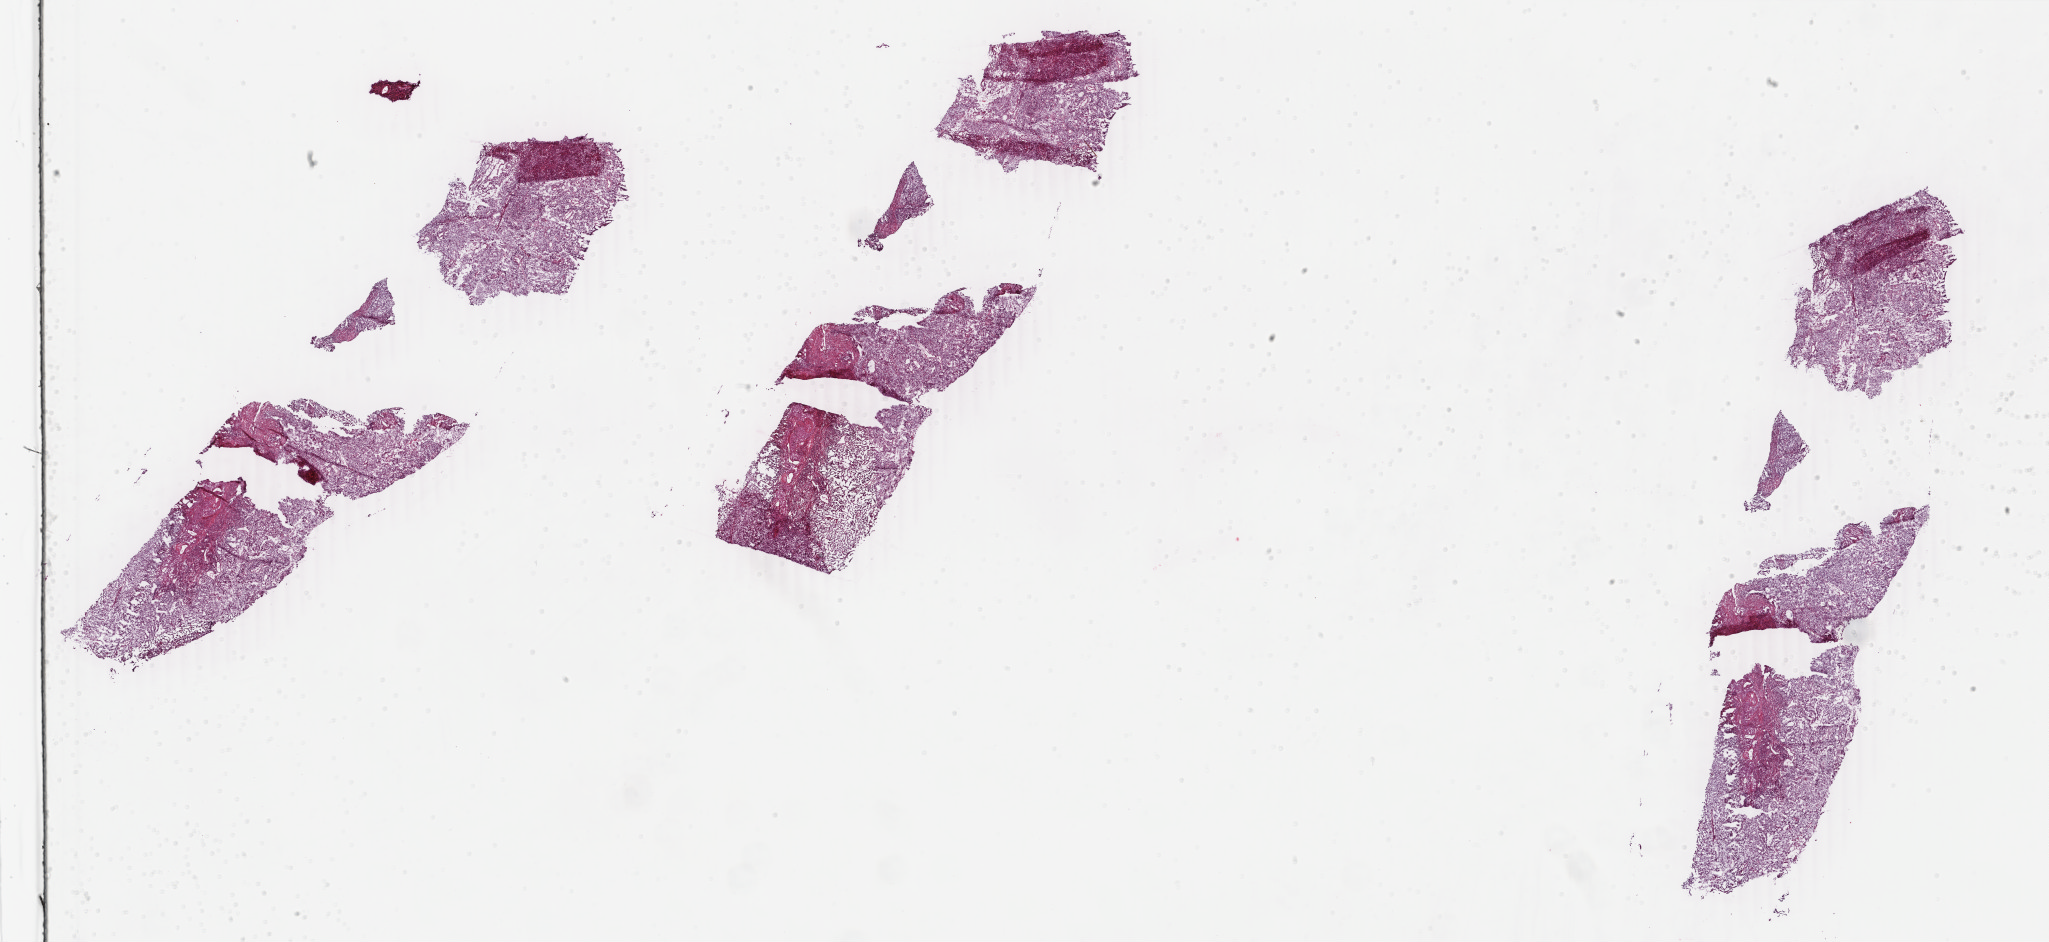
Digitized H&E-stained tissue section (whole slide), whole scanned area (about 32.6 x 15.0 mm) shown as a low-resolution overview. Frozen section. Primary tumour sample from the uterus. Female, age 81 years at initial diagnosis.
Diagnosis: Endometrioid adenocarcinoma, NOS.